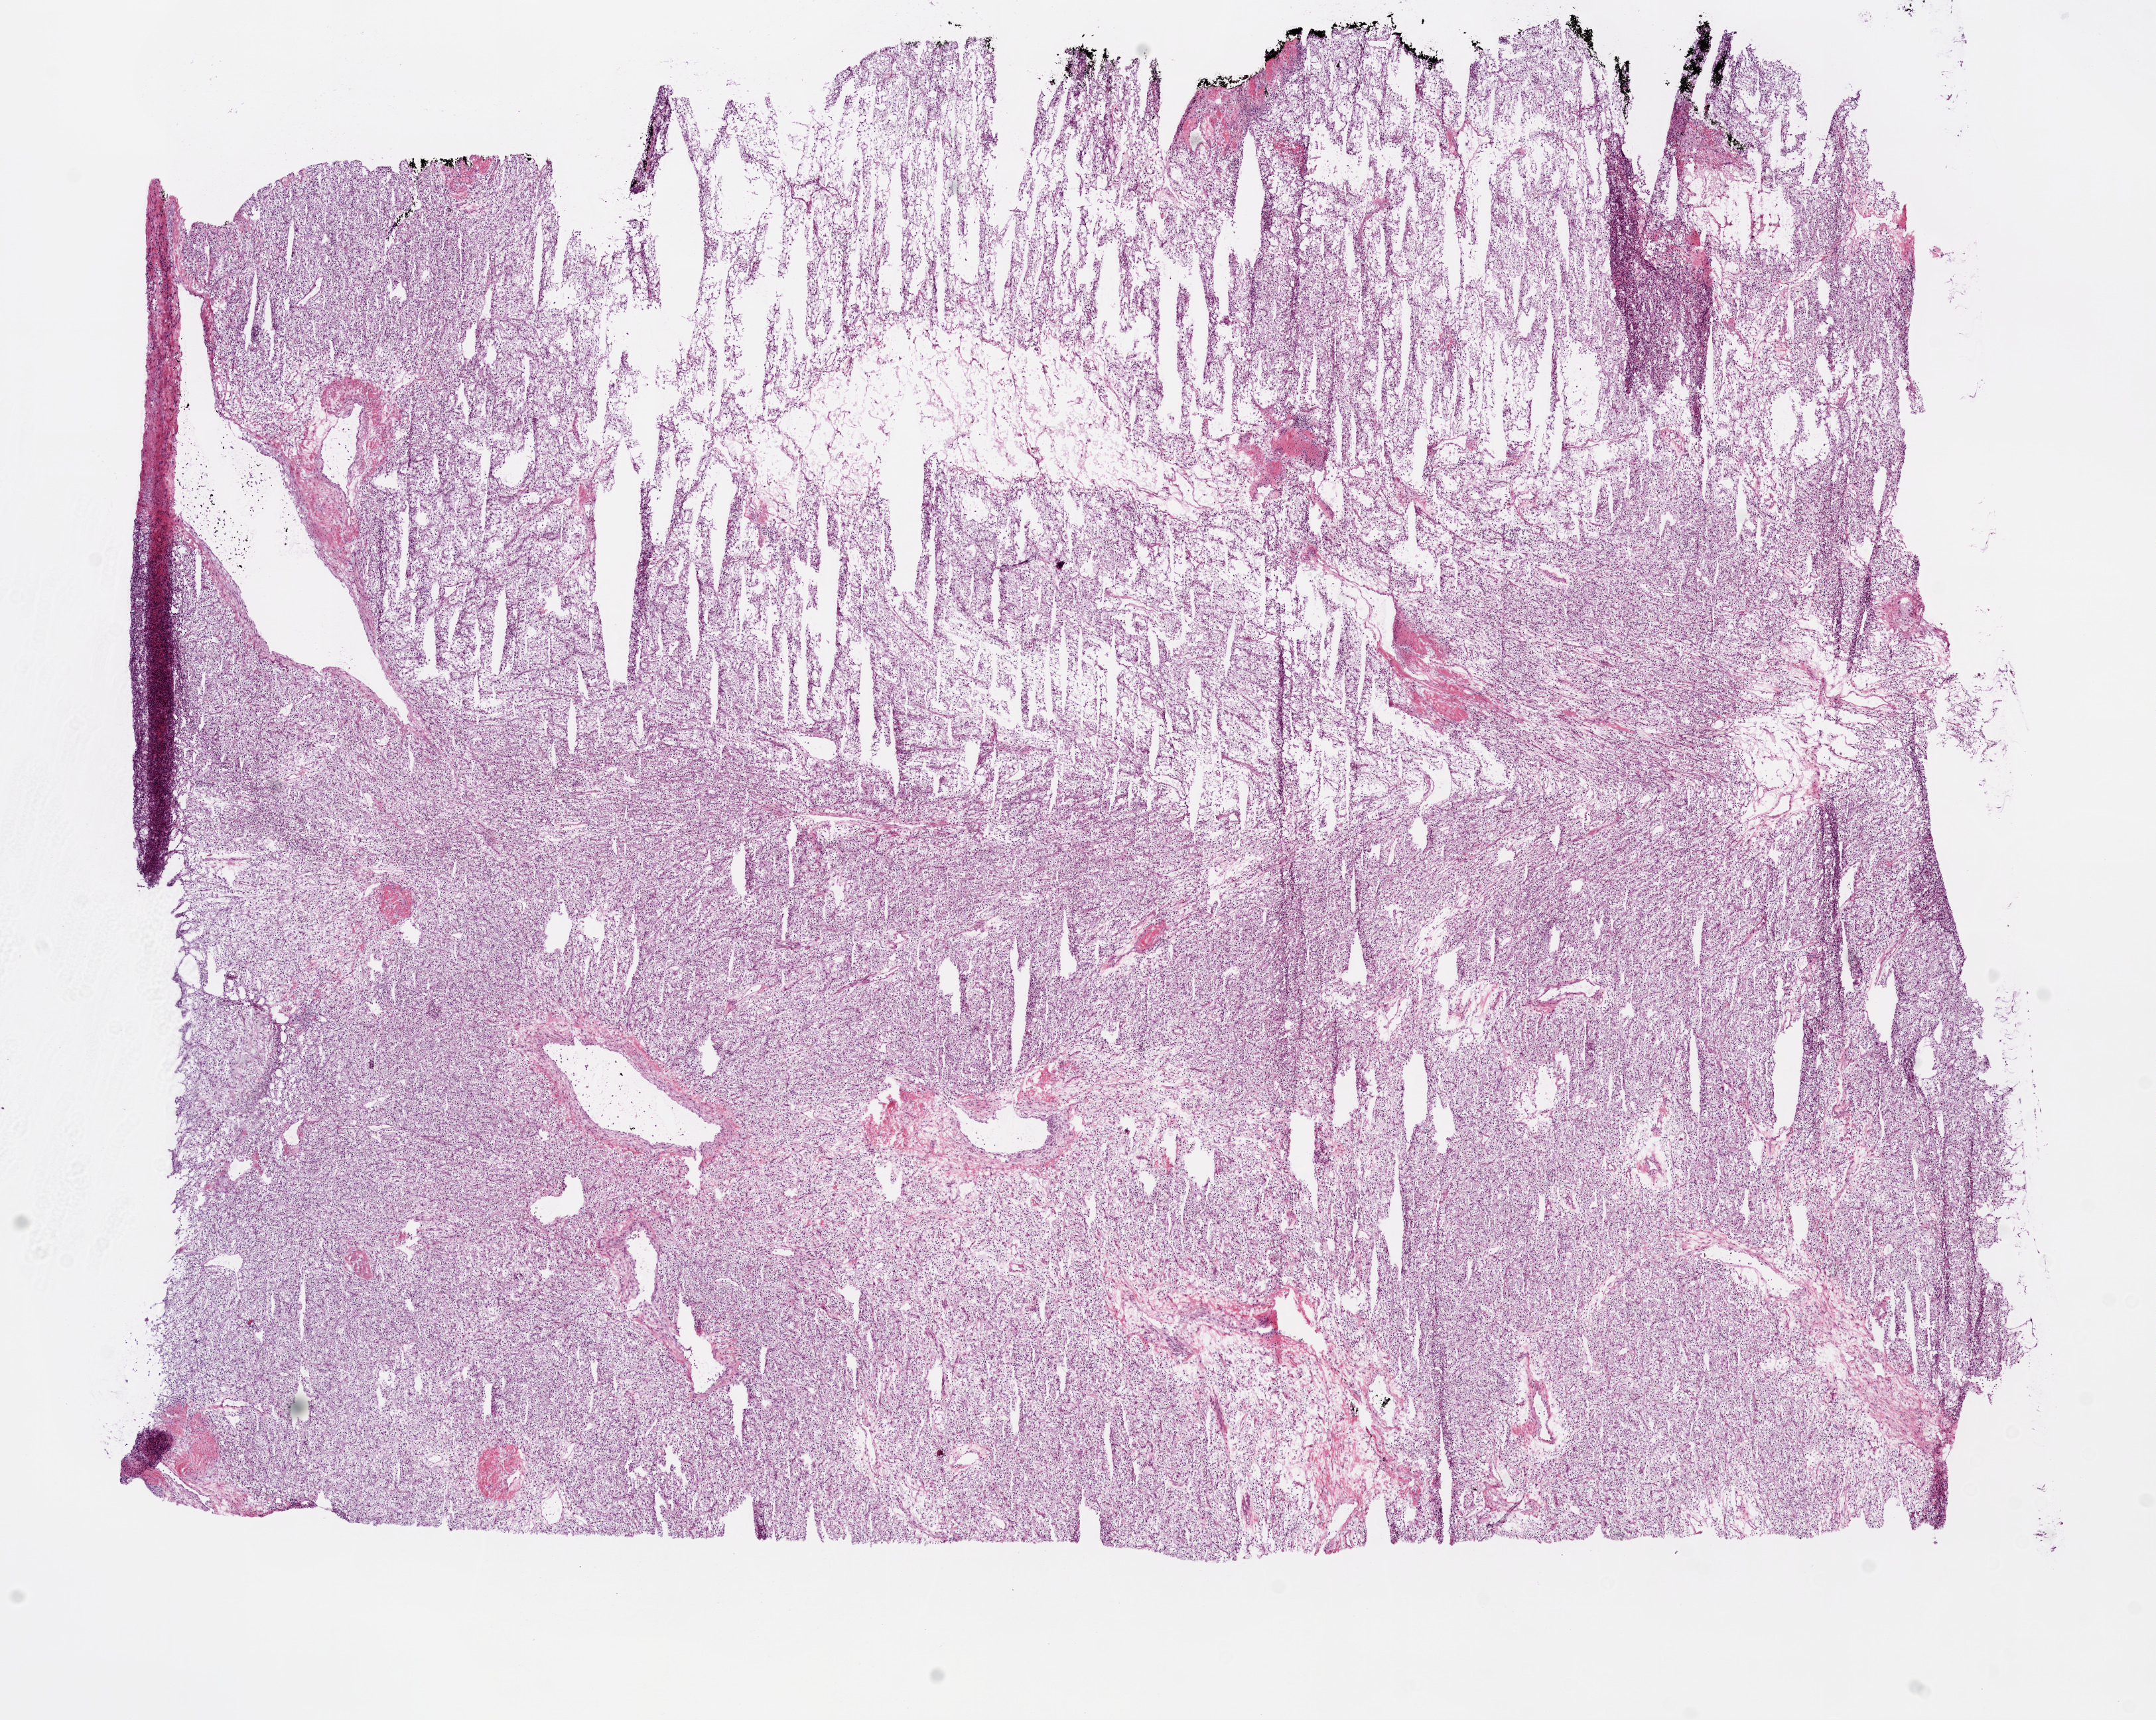
Whole-slide histology image, Hematoxylin and eosin (H&E) stained, shown as a low-resolution overview of the whole scanned area (about 13.0 x 10.4 mm, from a 20x scan); frozen section from the bottom of the tissue portion; primary tumour sample from the kidney. Male, age 53 years at initial diagnosis. Histologic grade: G1 (well differentiated). Slide review estimates, as recorded: tumour cells 95%, tumour nuclei 85%, normal cells 0%, stromal cells 5%, necrosis 0%.
• pathologic diagnosis: Clear cell adenocarcinoma, NOS
• AJCC pathologic stage: I